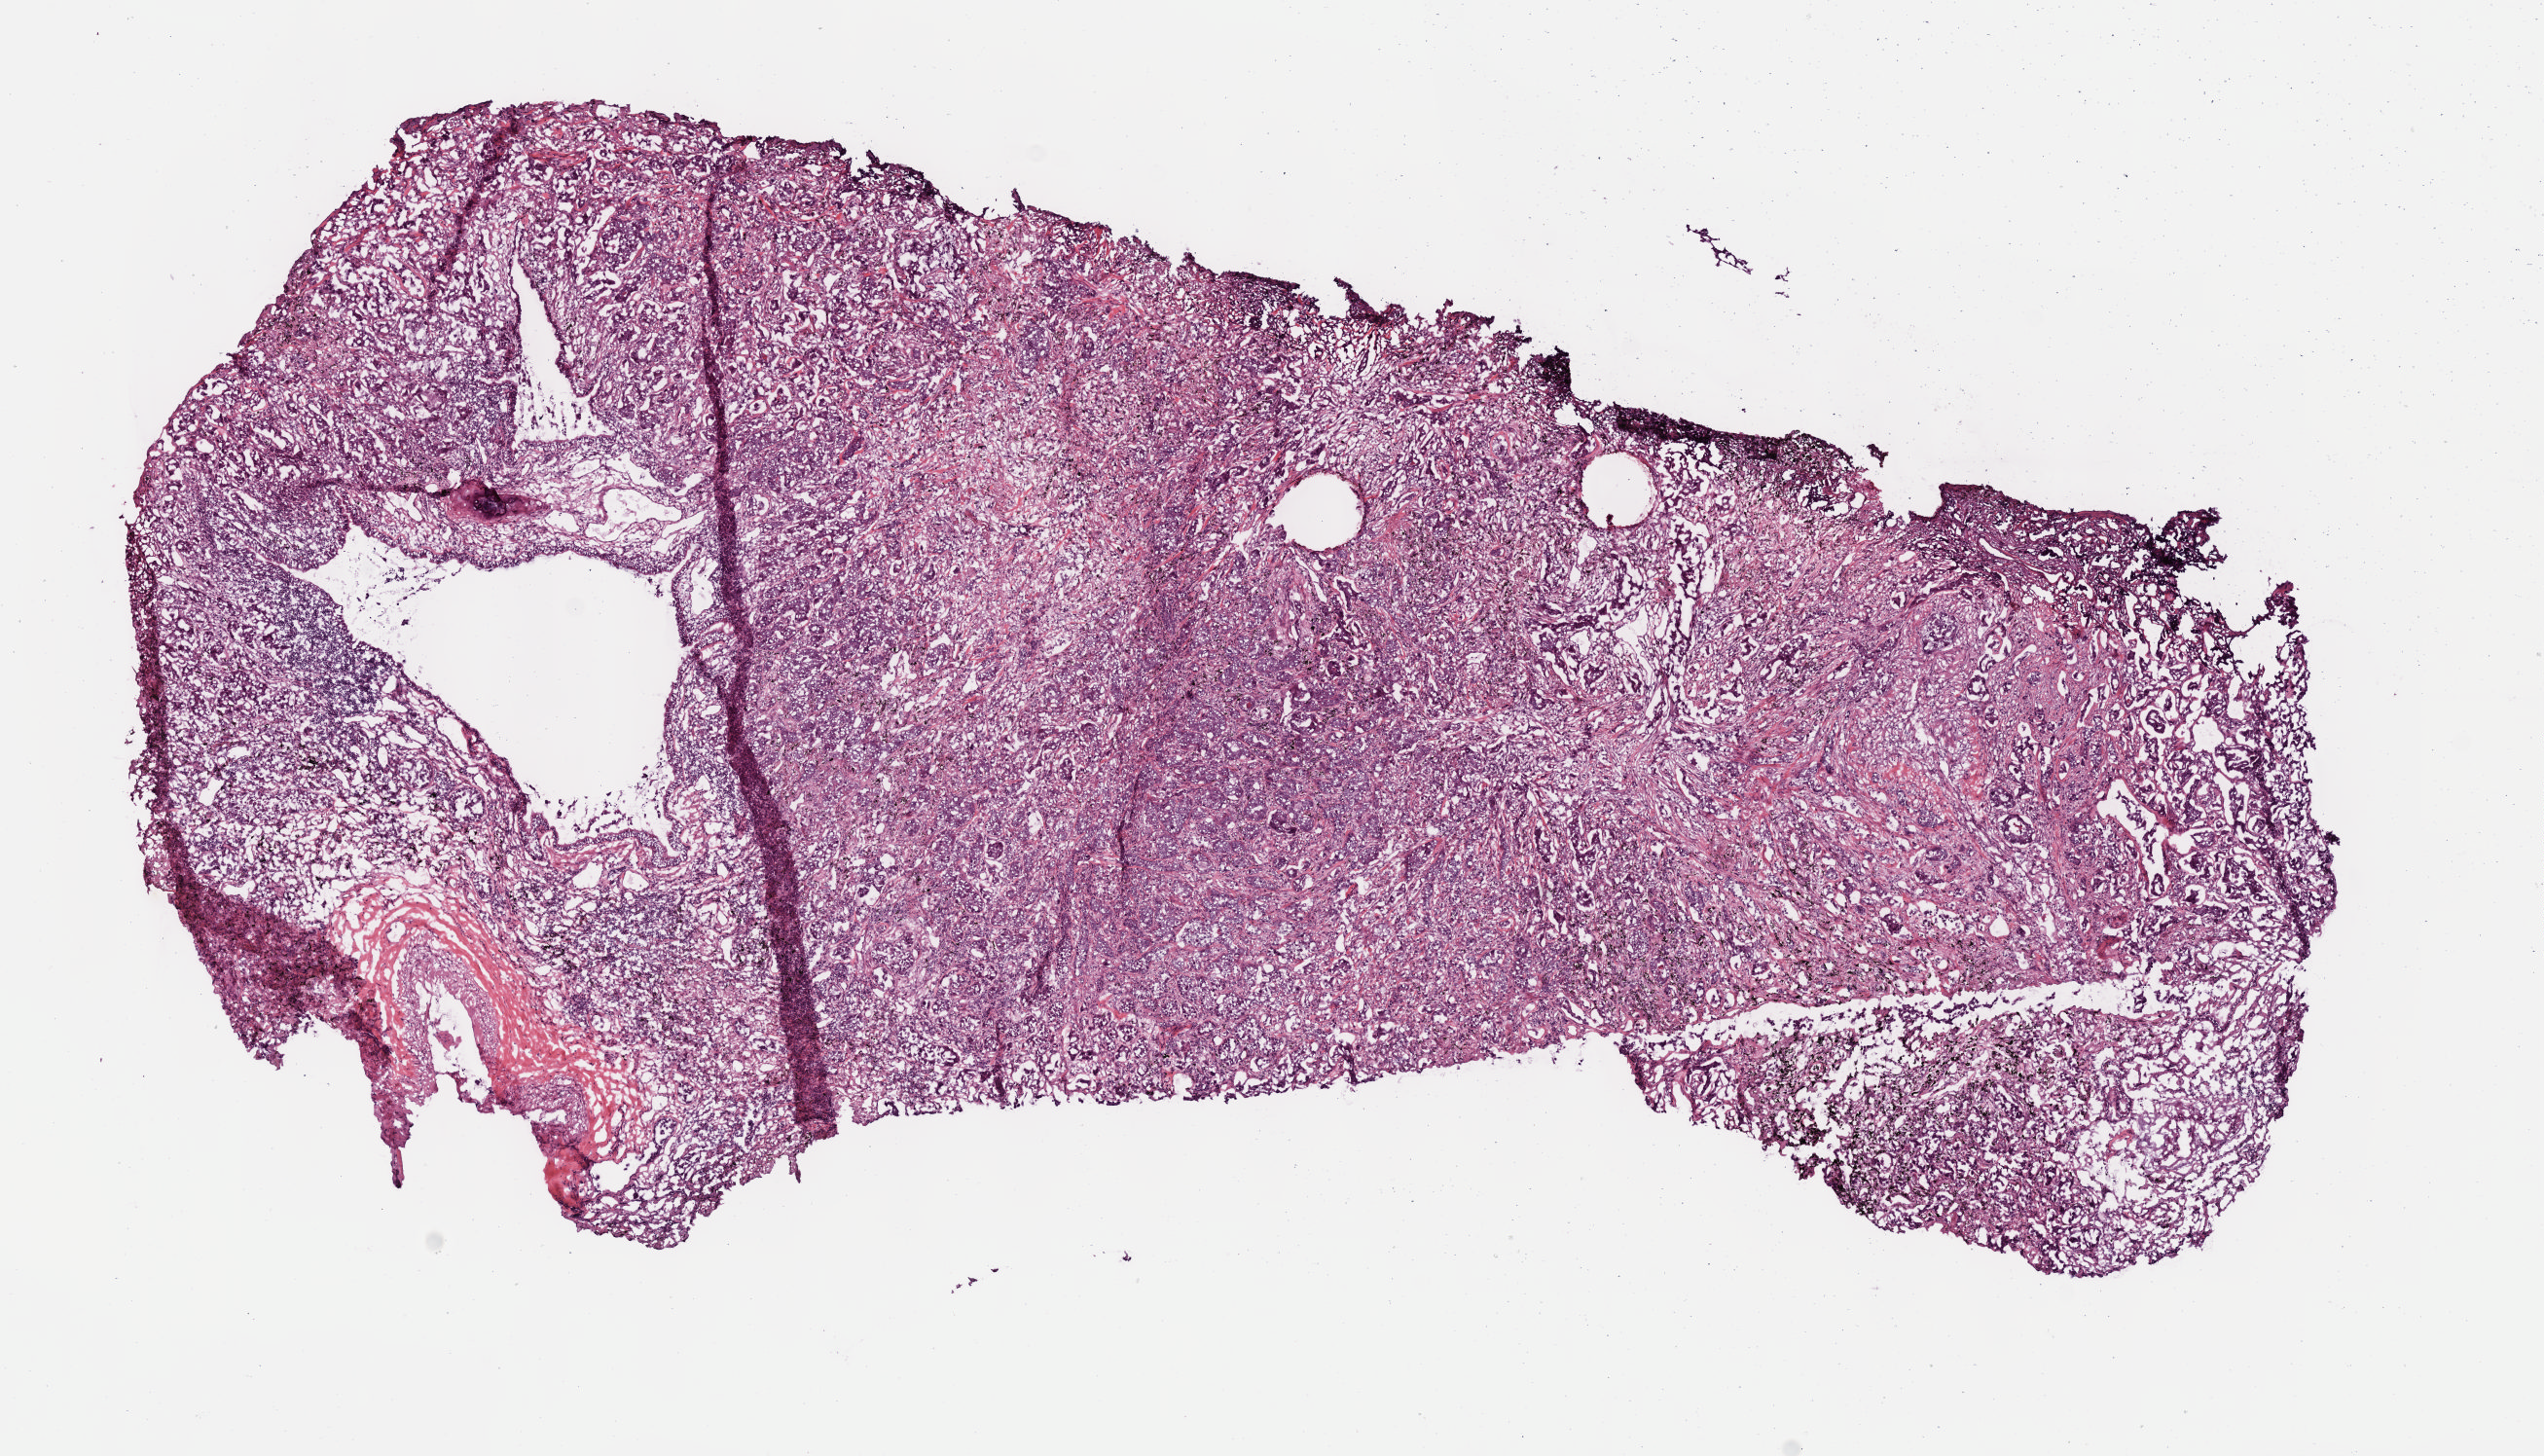
Digitized H&E tissue section (whole slide), low-resolution overview of the scanned area, about 10.6 x 6.0 mm (slide scanned at 40x), frozen section from the top of the tissue portion, lung, primary tumour sample. Female, age 72 years at initial diagnosis.
Histologic diagnosis: Adenocarcinoma, NOS (upper lobe, lung).